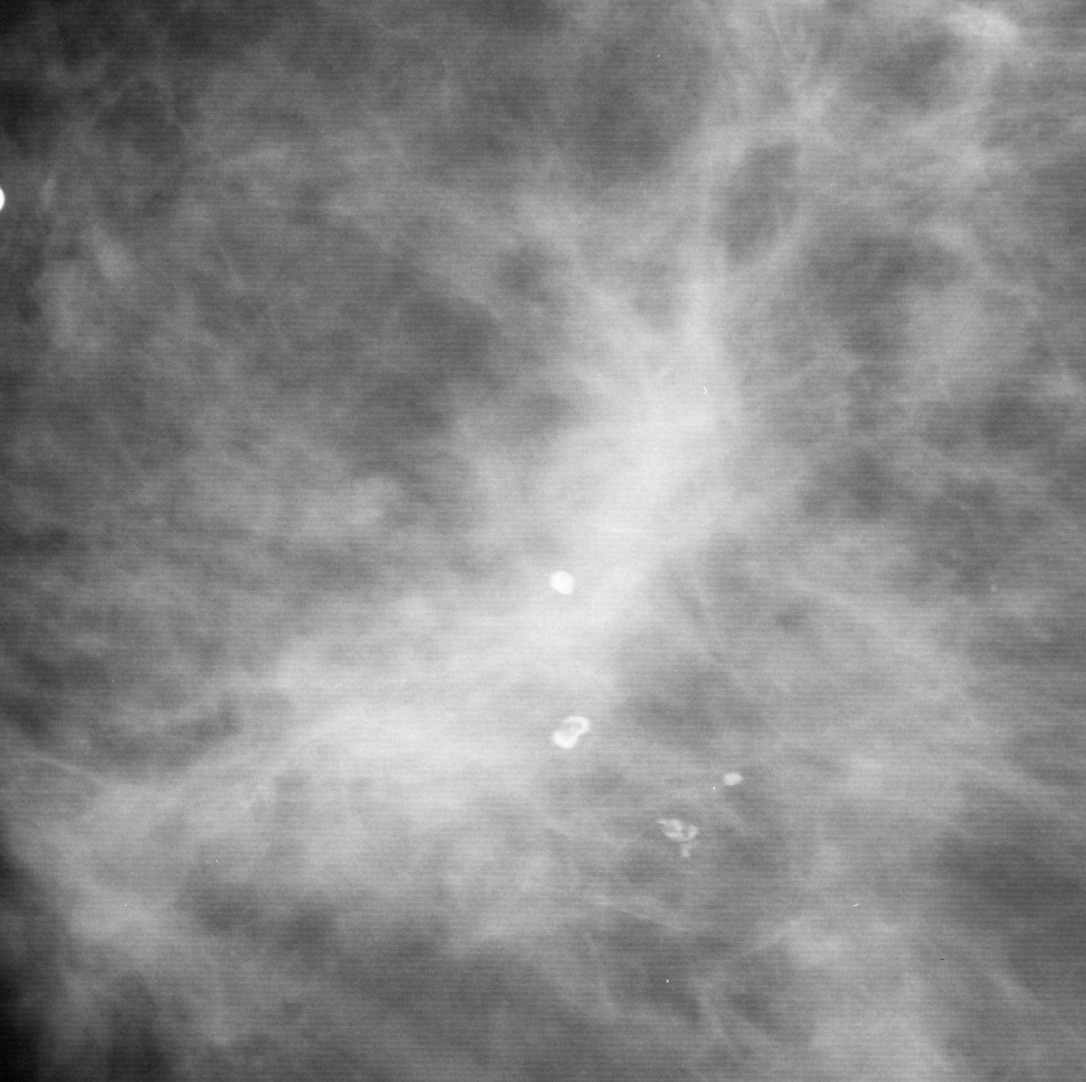
Crop from a digitized film mammogram around one marked abnormality, right breast, CC view.
- Marked abnormality: mass, shape asymmetric breast tissue, margins ill defined; BI-RADS assessment category 5; pathology result (as recorded, not read from the image): malignant.